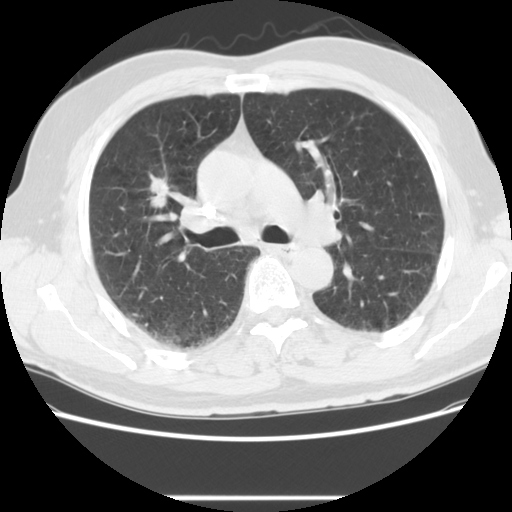
Low-dose screening chest CT, one axial slice. Position 85 of 139 along the scan axis. Lung window (W 1500 / L -600 HU). 2.5 mm slice thickness. 512 × 512 image matrix, field of view 360 × 360 mm.
Structures marked on this image (manually delineated by an expert):
- lesion 1 (tumor, upper lobe of right lung): bounding box [x1, y1, x2, y2] px = [149, 173, 169, 208]